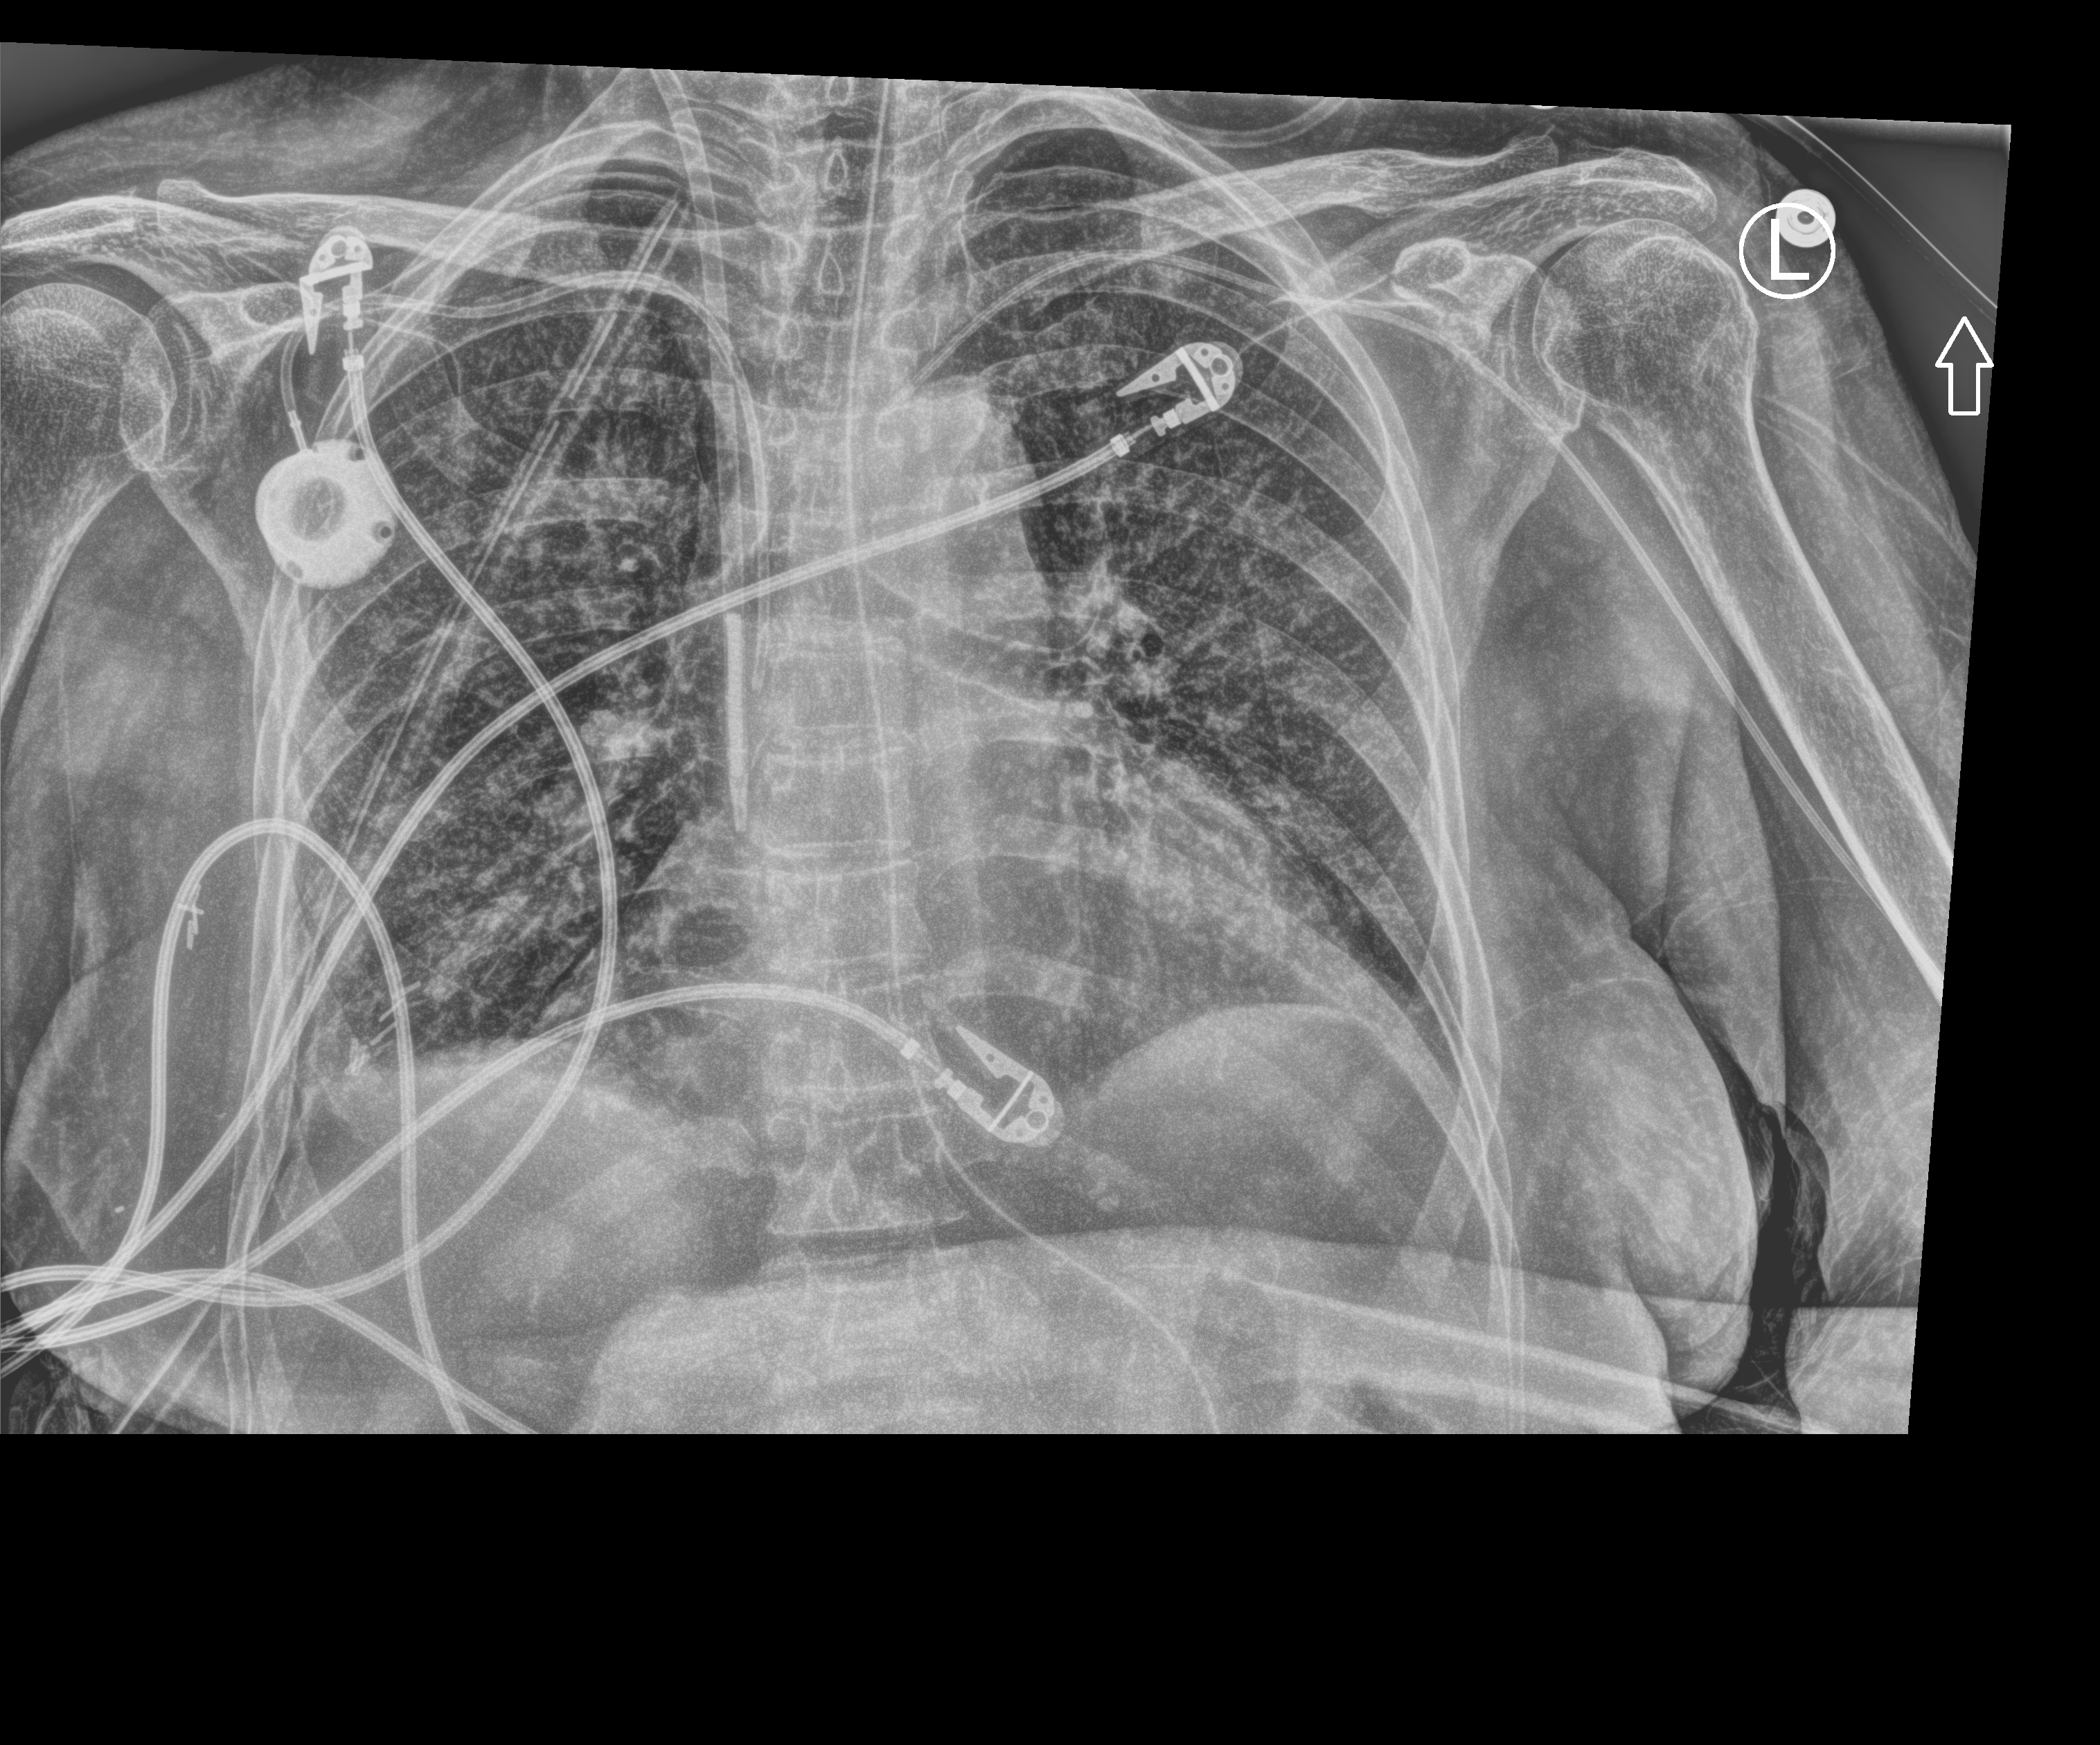
Portable chest radiograph, anteroposterior (AP) projection. Female patient hospitalised with COVID-19, age 60–74 years.
Hospital-stay facts (about this admission, not read from this image; timing relative to this image not recorded):
- diabetes (admission record): no
- admitted to intensive care during this hospital stay: yes